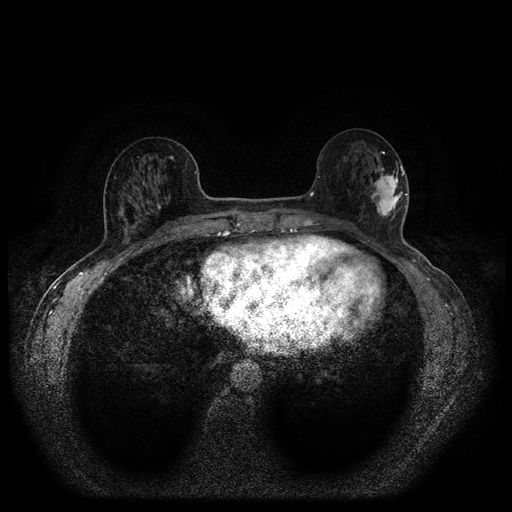
Breast MRI (dynamic contrast-enhanced, multi-phase), one axial slice. Position 42 of 116 along the scan axis. Dynamic contrast-enhanced series, time point 2 of 5 at this slice position (early post-contrast). 1.5 T. TE 2.7 ms, TR 5.4 ms. 2 mm slice thickness. 512 × 512 image matrix. Patient: female, 56 years.
Outlined on this slice (semi-automatically segmented with operator editing):
- breast lesion (labelled 'tumour' in the annotation; benign lesions carry a separate 'benign' label): box from (x=368, y=160) to (x=405, y=219) px